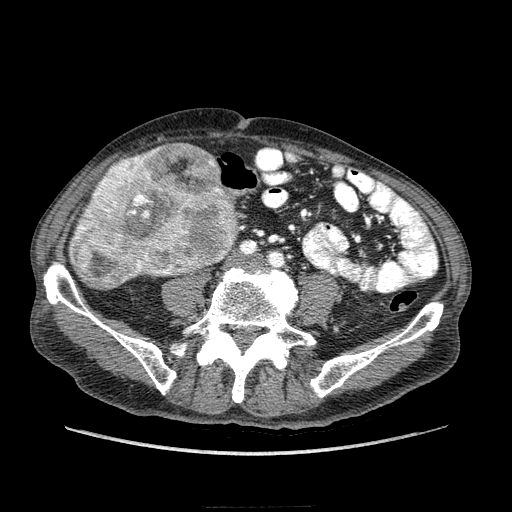
Contrast-enhanced abdominal CT (liver protocol), one axial slice; position 35 of 218 along the scan axis; reconstruction kernel STANDARD; 100 kVp; soft-tissue window (W 400 / L 40 HU); 512 × 512 image matrix, field of view 380 × 380 mm. Case-level facts recorded for this patient, not image findings: diagnosis: hepatocellular carcinoma (patient treated with transarterial chemoembolisation; whether this scan precedes or follows treatment is not stated here); TNM stage (as recorded): Stage-IIIA; Child-Pugh class: A; tumour differentiation: well differentiated; tumour nodularity: multinodular.
Outlined on this slice (semi-automatic segmentation, software-assisted and operator-edited):
- liver parenchyma outside the tumour (the mass and vessels are separate outlines, so this box may not span the whole liver): bounding box (x1, y1, x2, y2) in pixels: (74, 180, 101, 234)
- mass: (68, 142, 242, 290)